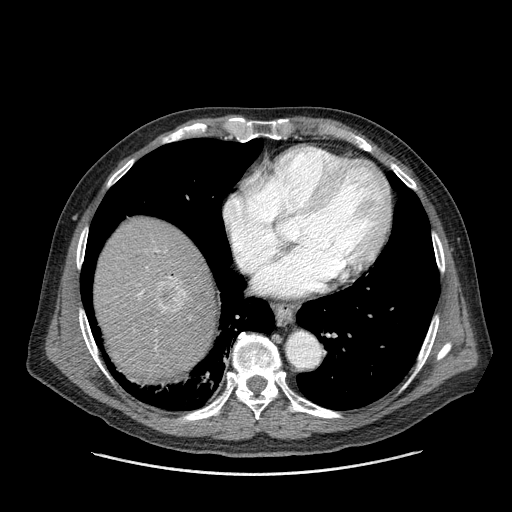
Contrast-enhanced abdominal CT (liver protocol), one axial slice. Position 144 of 180 along the scan axis. Reconstruction kernel STANDARD. 120 kVp. One of 2 acquisitions stored at this slice position. Soft-tissue window (W 400 / L 40 HU). 2.5 mm slice thickness. 512 × 512 image matrix. Case-level facts recorded for this patient, not image findings: diagnosis: hepatocellular carcinoma (patient treated with transarterial chemoembolisation; whether this scan precedes or follows treatment is not stated here); TNM stage (as recorded): Stage-II; Child-Pugh class: A; tumour differentiation: well differentiated; tumour nodularity: multinodular.
Annotated regions visible in this slice (semi-automatic segmentation, software-assisted and operator-edited):
- abdominal aorta: box from (x=288, y=334) to (x=320, y=367) px
- liver parenchyma outside the tumour (the mass and vessels are separate outlines, so this box may not span the whole liver): (x=94, y=216)–(x=216, y=382)
- mass: (x=154, y=276)–(x=187, y=314)
- liver vessels: (x=138, y=290)–(x=144, y=295)